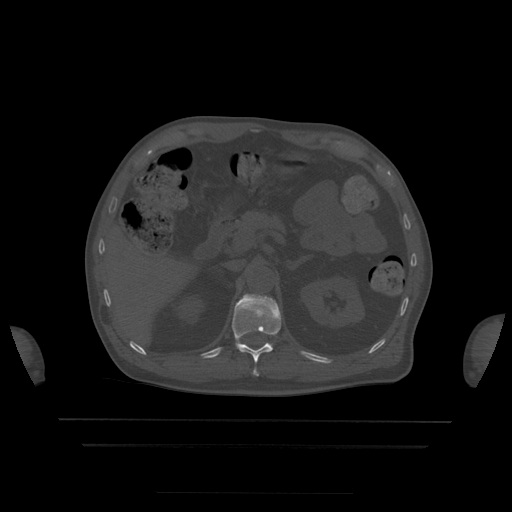
CT including the spine, one axial slice; slice 192 of 522 in the series (ordered by position); bone window (W 1800 / L 400 HU); 1.25 mm slice thickness; 512 × 512 image matrix, field of view 436 × 436 mm. Patient age 68 years. From the clinical record (not read from this slice): primary cancer: urothelial.
Annotated regions visible in this slice (semi-automatically segmented with operator editing):
- L1 vertebra: bounding box [x1, y1, x2, y2] px = [261, 296, 276, 303]
- T12 vertebra: [232, 295, 282, 376]